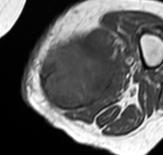
MRI of an extremity soft-tissue mass, one axial slice; position 23 of 65 along the scan axis; MR volume resampled by the dataset authors to the PET/CT grid (not the native acquisition matrix); 163 × 155 image matrix. Female patient. From the clinical record (not read from this slice): histological type: pleomorphic leiomyosarcoma; grade: high; site of the primary tumour: left thigh.
Structures marked on this image (expert contour drawn on MRI and transferred to this co-registered scan by the dataset authors):
- gross tumour volume including surrounding oedema: bounding box [x1, y1, x2, y2] px = [39, 31, 122, 112]
- gross tumour volume (mass): [39, 44, 116, 111]